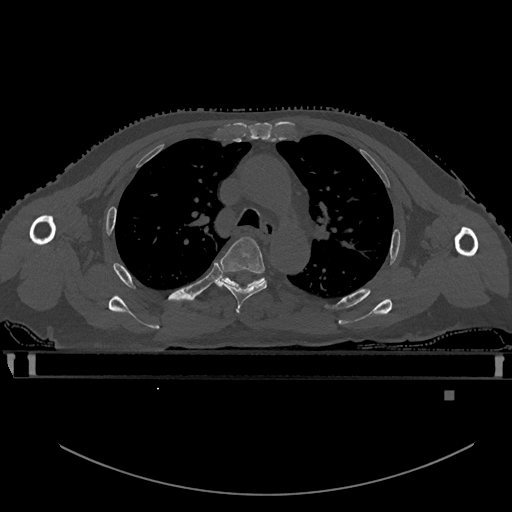
CT including the spine, one axial slice; slice 394 of 969 in the series (ordered by position); bone window (W 1800 / L 400 HU); 512 × 512 image matrix. Patient: male, 82 years. From the clinical record (not read from this slice): primary cancer: prostate.
Outlined on this slice (semi-automatic segmentation, software-assisted and operator-edited):
- T4 vertebra: bounding box <216,236,267,312> (left, top, right, bottom; pixels)
- T5 vertebra: <219,274,265,286>